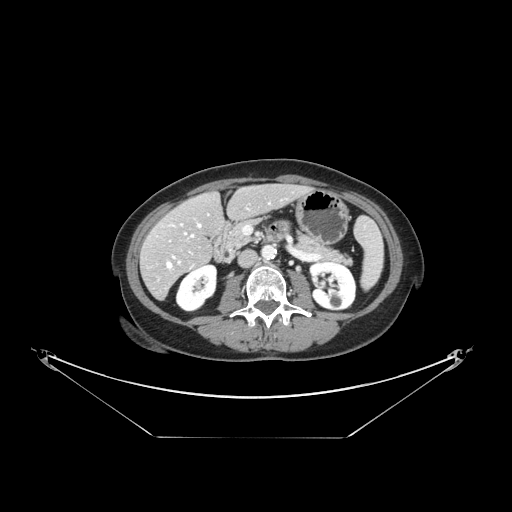
Contrast-enhanced abdominal CT, one axial slice; position 57 of 148 along the scan axis; reconstruction kernel STANDARD; 120 kVp; intravenous contrast given; soft-tissue window (W 400 / L 40 HU); 512 × 512 image matrix. Female patient, age 73 years. Case-level facts recorded for this patient, not image findings: diagnosis: colorectal cancer liver metastases, imaged before liver resection; multiple liver metastases: no; largest metastasis: 1 cm.
Outlined on this slice (expert manual segmentation):
- hepatic veins: bounding box <167,224,201,268> (left, top, right, bottom; pixels)
- liver: <142,185,306,298>
- planned liver remnant (the part of the liver to remain after resection): <164,185,306,248>